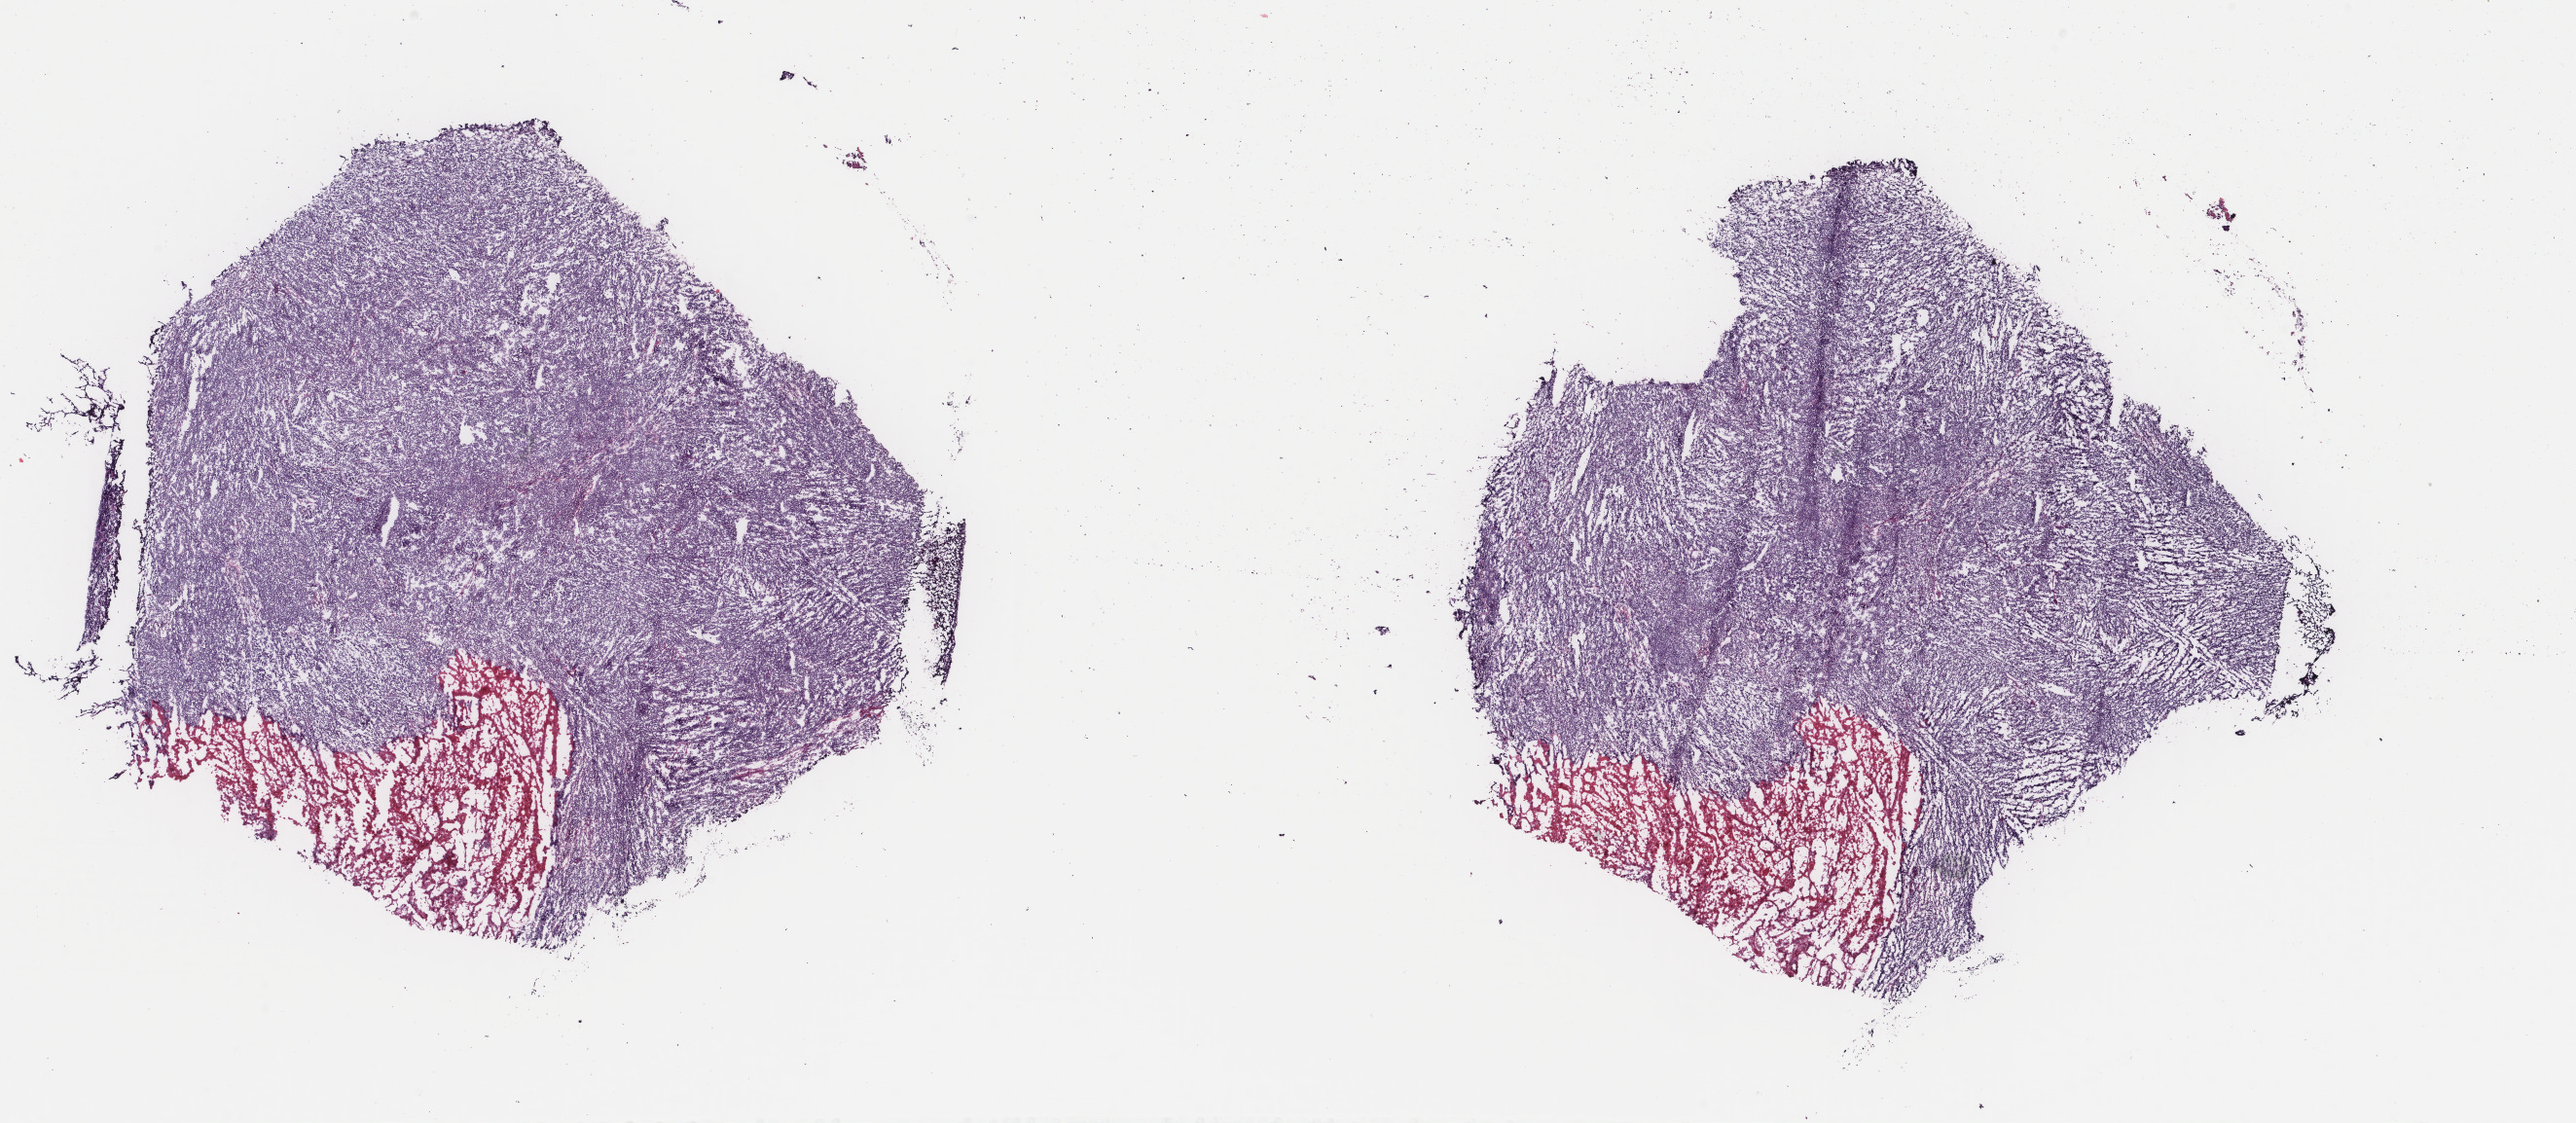
H&E whole-slide image, whole scanned area (about 21.0 x 9.2 mm) shown as a low-resolution overview; frozen section; primary tumour sample from the uterus. Female patient; age at initial diagnosis 74 years. Histologic grade: G3 (poorly differentiated). Composition of this section per pathologist review: tumour cells 83%, tumour nuclei 98%, normal cells 0%, stromal cells 2%, necrosis 15%. Infiltration values recorded for this section: lymphocyte infiltration 15%, monocyte infiltration 5%, neutrophil infiltration 3%.
• FIGO stage: IB
• pathologic diagnosis: Endometrioid adenocarcinoma, NOS (endometrium)